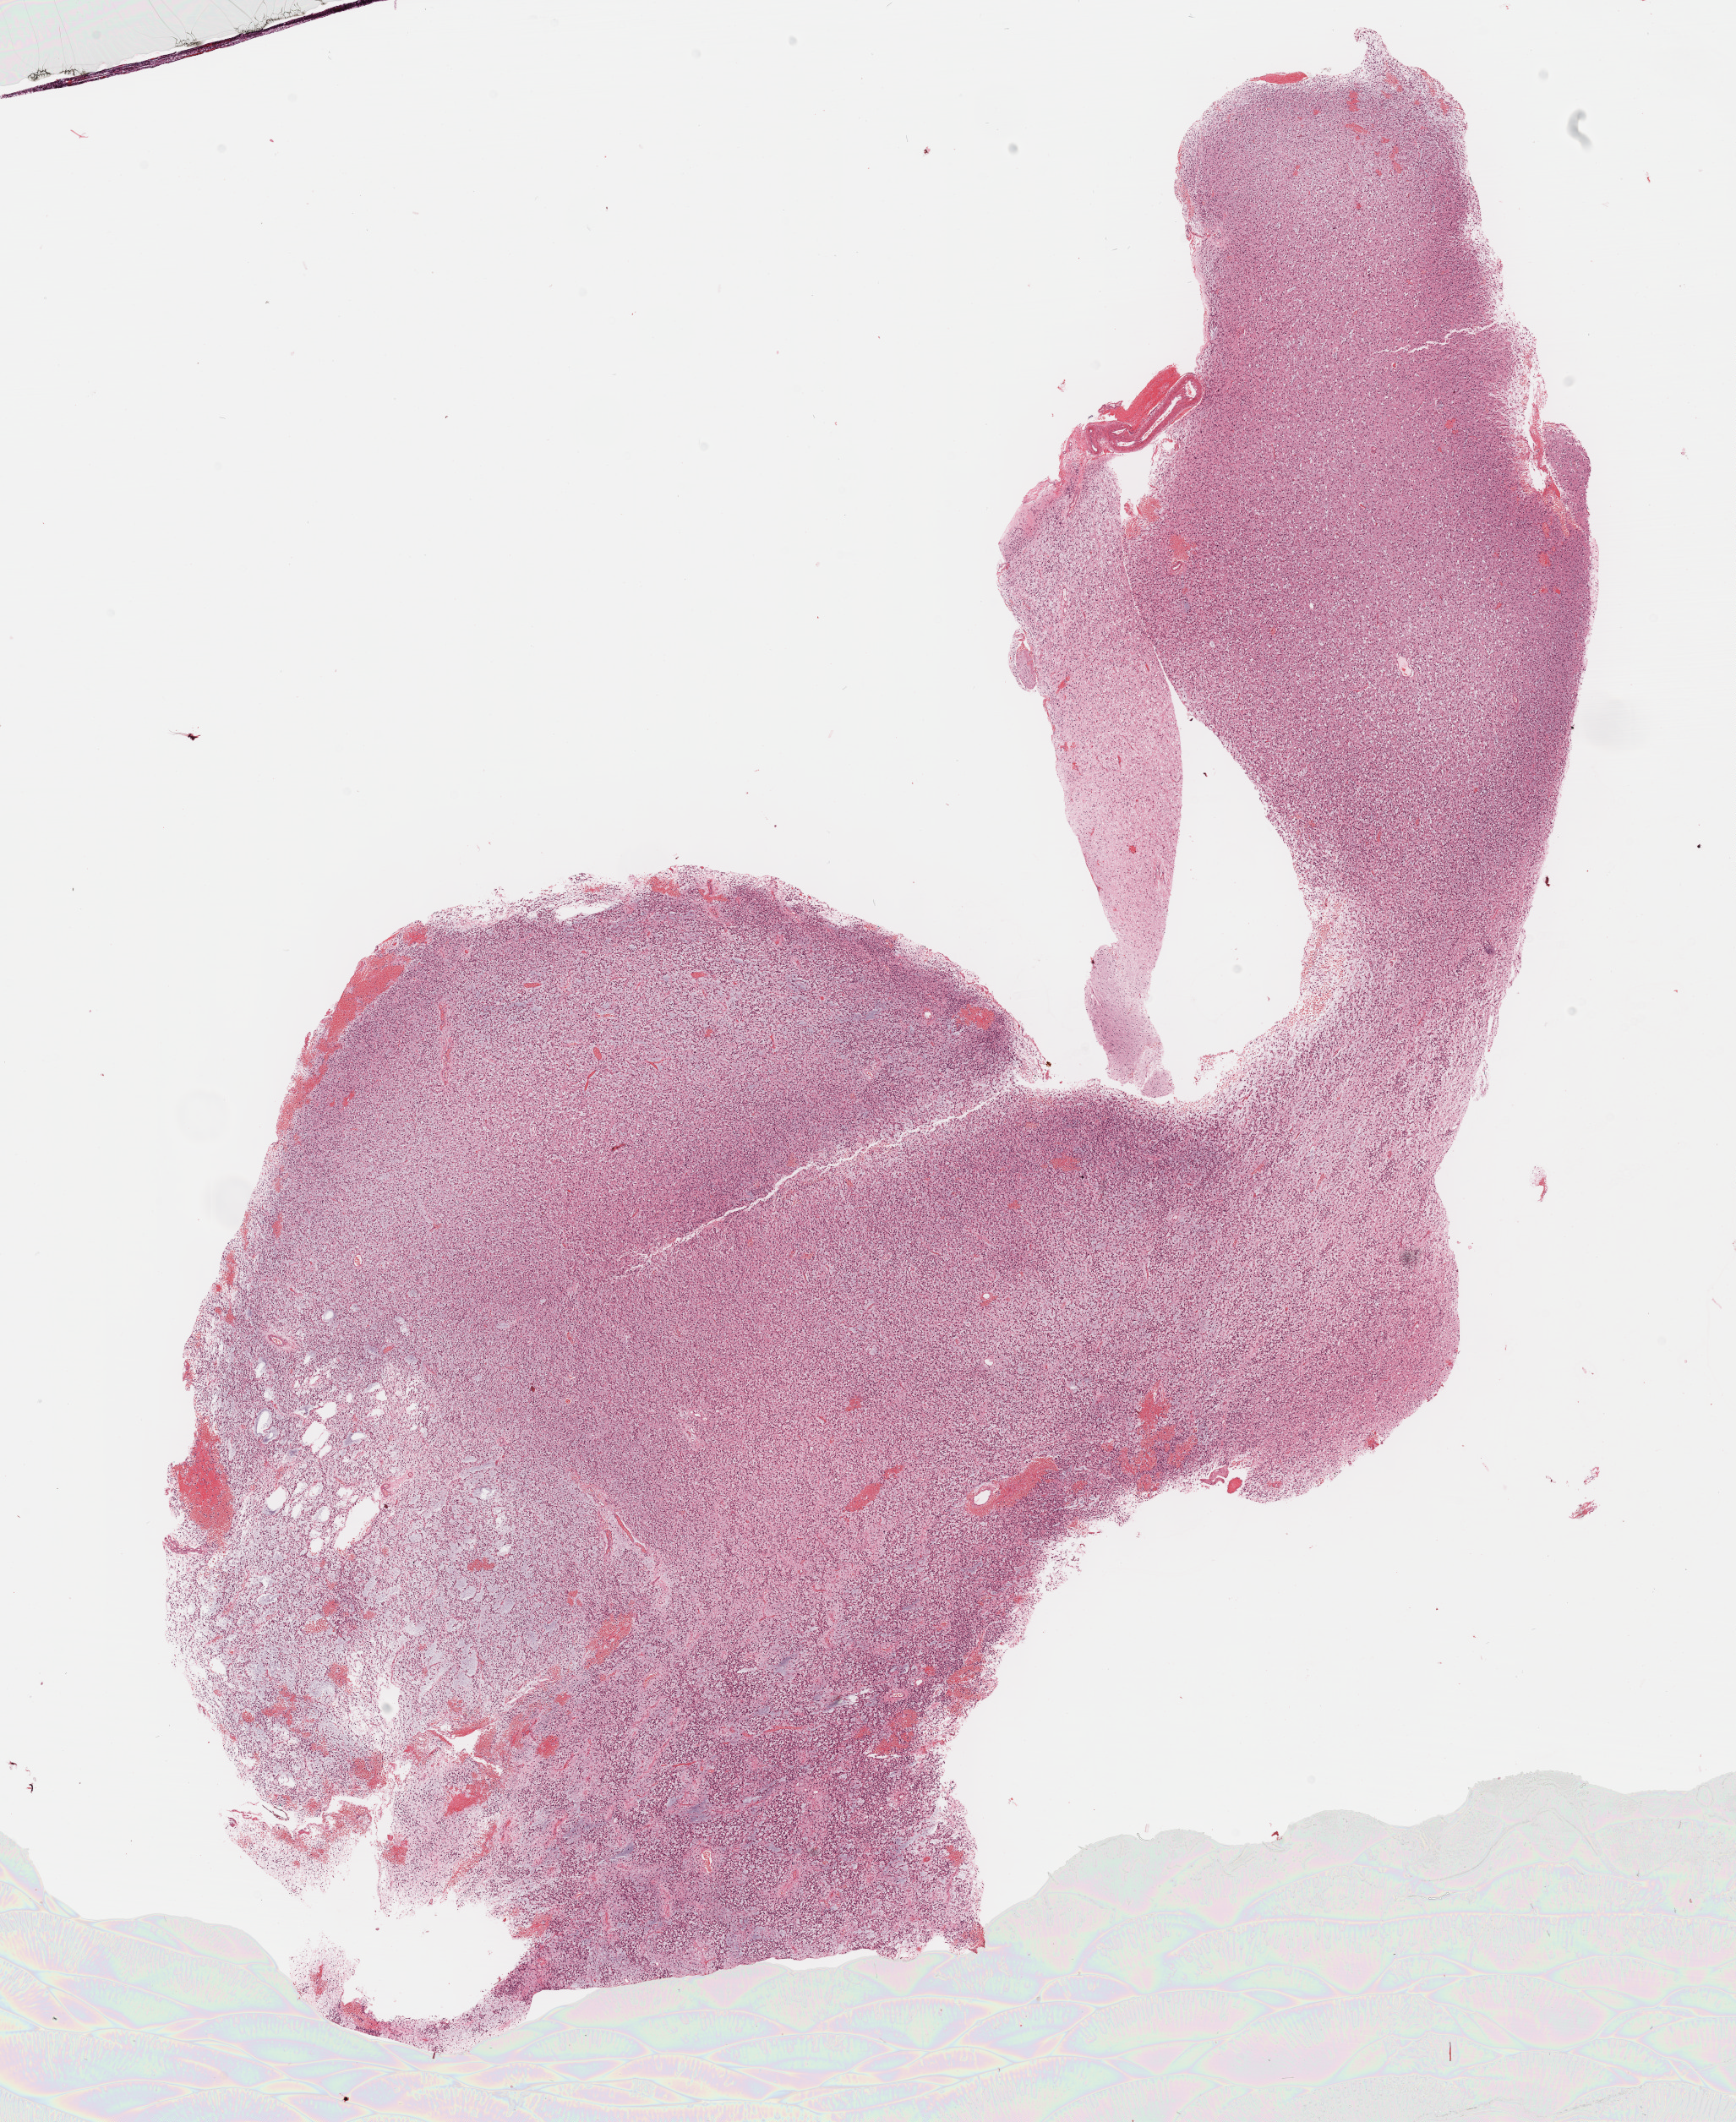
Whole-slide histology image, H&E, low-resolution overview of the scanned area, about 16.6 x 20.3 mm. FFPE section. Primary tumour sample from the brain. Patient: female, age at initial diagnosis 44 years. Histologic grade: G3 (poorly differentiated).
Laterality: right. Pathologic diagnosis: Mixed glioma (cerebrum).